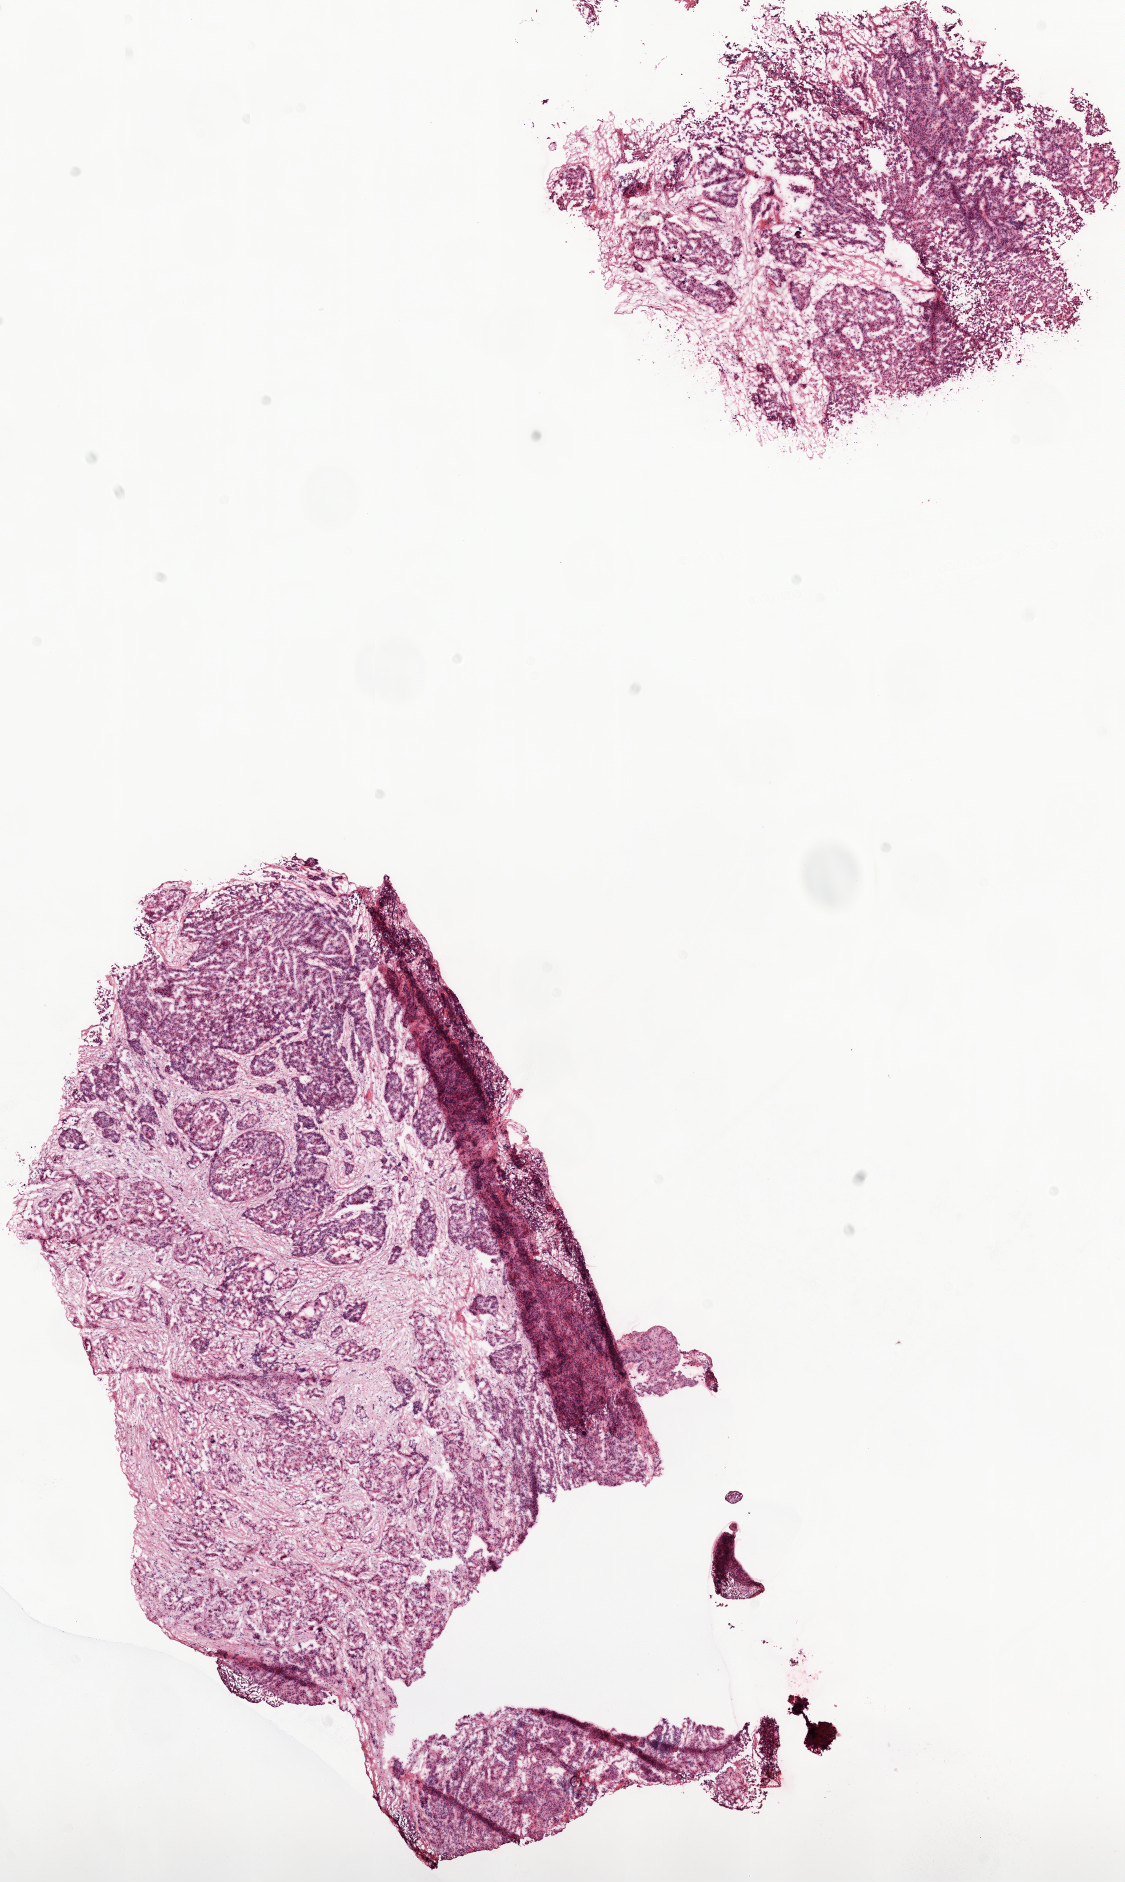
Digitized H&E-stained tissue section (whole slide) — low-resolution overview of the scanned area, about 9.0 x 15.1 mm; frozen section from the top of the tissue portion; ovary, primary tumour sample. Patient: female, age at initial diagnosis 46 years. Histologic grade: G3 (poorly differentiated). Slide review estimates, as recorded: tumour cells 65%, tumour nuclei 85%, normal cells 0%, stromal cells 35%, necrosis 0%.
Pathologic diagnosis: Serous cystadenocarcinoma, NOS. FIGO stage: IV.